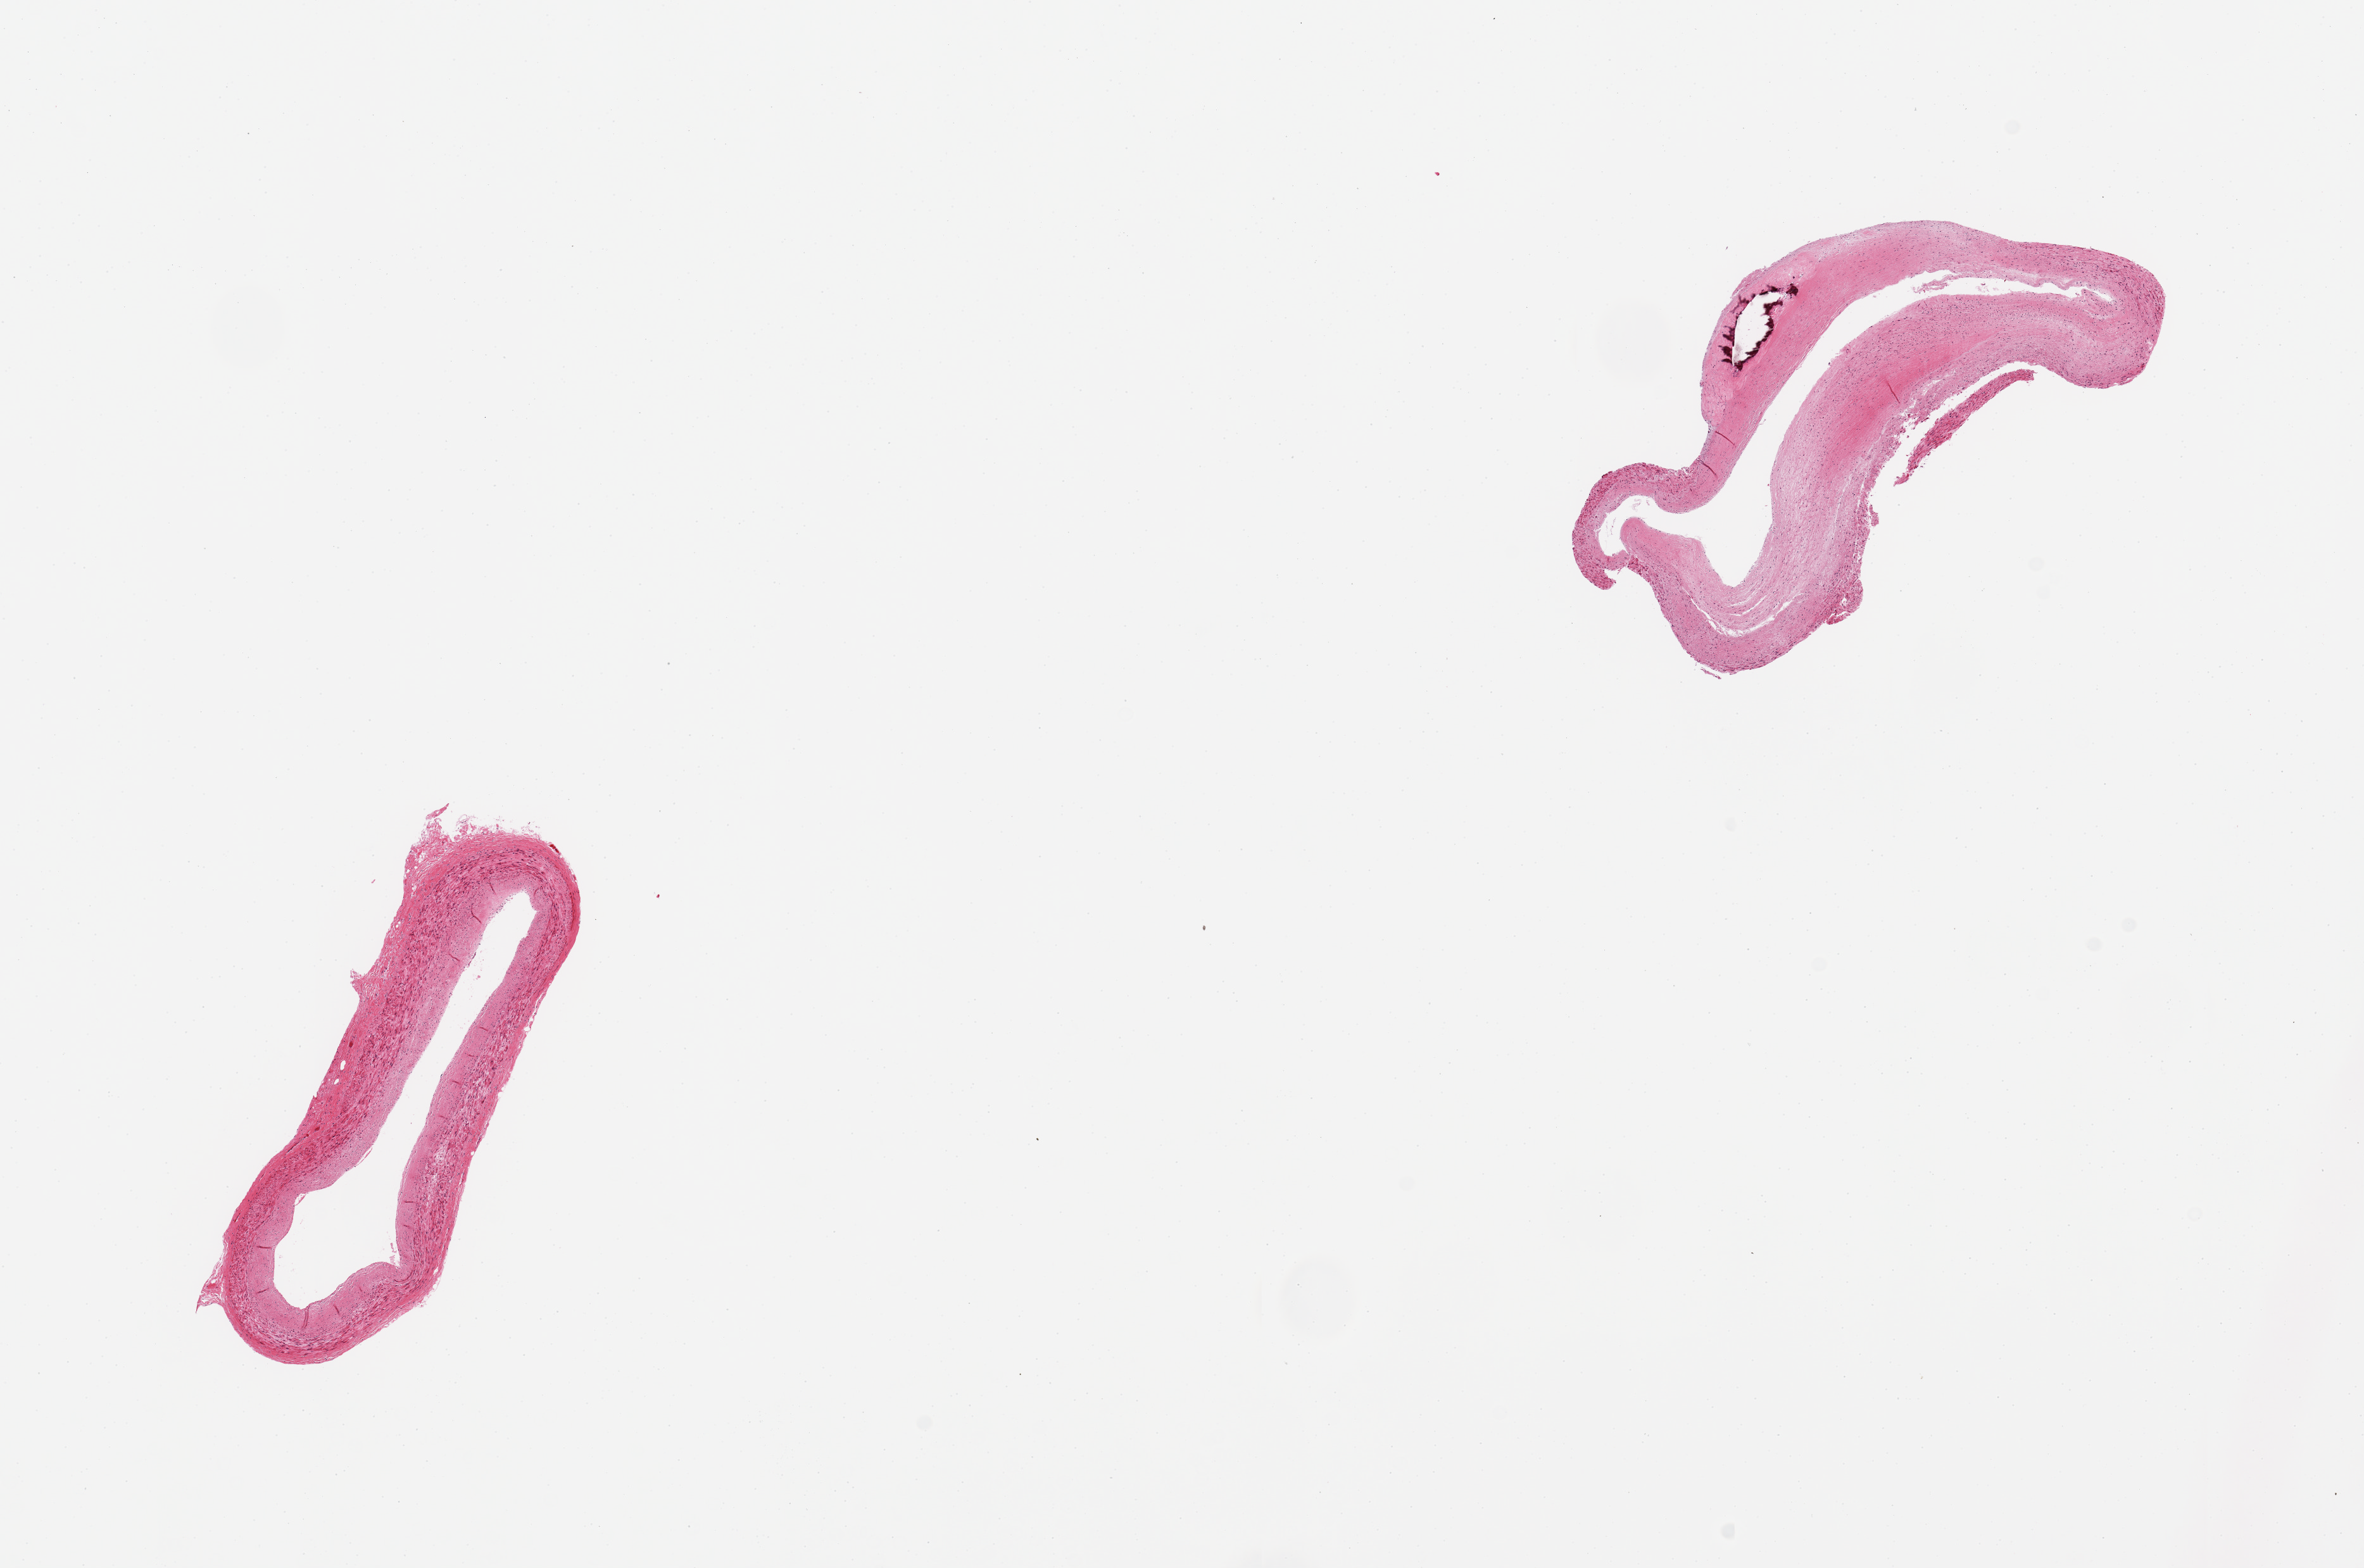
Whole-slide image, hematoxylin and eosin (H&E) stain, whole scanned area (about 14.8 x 9.8 mm) shown as a low-resolution overview; PAXgene-fixed, paraffin-embedded tissue; section of coronary artery (target tissue); donor tissue sample. Donor sex: male.
- review note (as recorded): 2 pieces; extensive fibrocalcific plaques in 1, less in the other; well trimmed